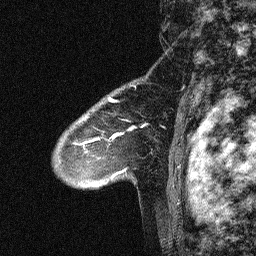
Breast MRI (dynamic contrast-enhanced), one sagittal slice. Slice 47 of 64 in the series (ordered by position). Dynamic contrast-enhanced study with each time point stored as its own series, time point 2 of 3 at this slice position (early post-contrast, ordered by acquisition time). 1.5 T. TE 4.5 ms, TR 11 ms. 256 × 256 image matrix, field of view 200 × 200 mm. Patient: female, 46 years. Case-level facts recorded for this patient, not image findings: setting: breast cancer imaged before/during neoadjuvant chemotherapy; receptor status: HER2-positive.
Outlined on this slice (semi-automatic segmentation, software-assisted and operator-edited):
- analysis volume of interest (the breast-tissue region the enhancement analysis was run in; not a lesion): bounding box <42,80,150,180> (left, top, right, bottom; pixels)
- tumour enhancement mask (voxels above the 90 % enhancement threshold inside the analysis volume of interest): <74,100,149,148>